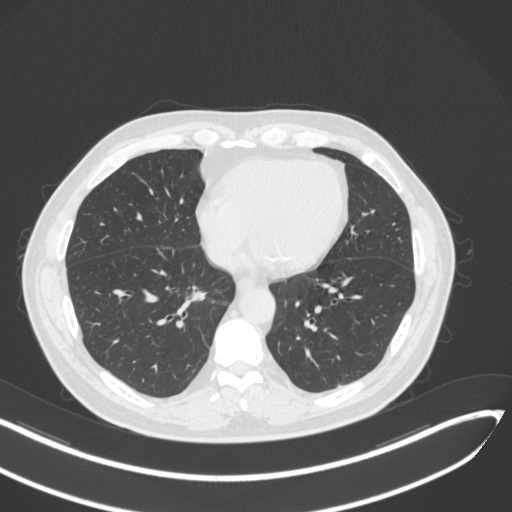
Chest CT, one axial slice; position 137 of 429 along the scan axis; 120 kVp; lung window (W 1500 / L -600 HU); 1 mm slice thickness; 512 × 512 image matrix, field of view 400 × 400 mm. Male patient, age 62 years. Case-level facts recorded for this patient, not image findings: clinical TNM (as recorded): T1b N0 M0; histopathological grade: G2.
Outlined on this slice (bounding box drawn by a radiologist):
- lung tumour (recorded histology: adenocarcinoma): bounding box [x1, y1, x2, y2] px = [187, 287, 210, 306]